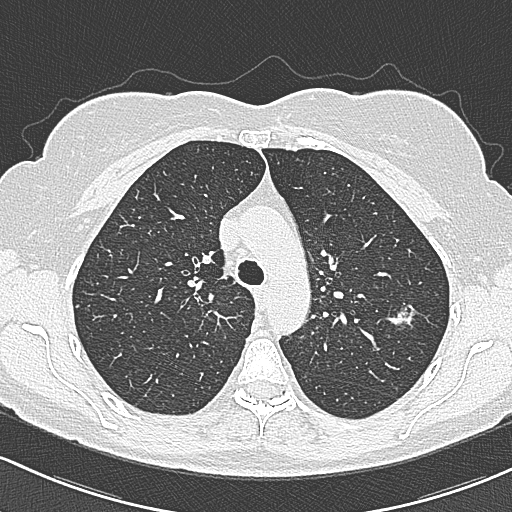
Axial slice from a low-dose chest CT screening exam, baseline screening round, lung window (W 1500 / L -600 HU), 1 mm slice thickness, slice 89 of 312 in the series. Female, age 65 years at enrolment. Current smoker at enrolment.
Lesion marked by an expert reader, box from (x=384, y=299) to (x=424, y=337) px. The screening reader recorded 3 non-calcified nodules or masses ≥4 mm on this exam (left upper lobe, left upper lobe, right upper lobe); which of them this box marks is not recorded. Later outcome: lung cancer diagnosed 390 days after this screen — bronchiolo-alveolar carcinoma, non-mucinous, left upper lobe, stage IA (AJCC 6th edition), 10 mm at pathology.